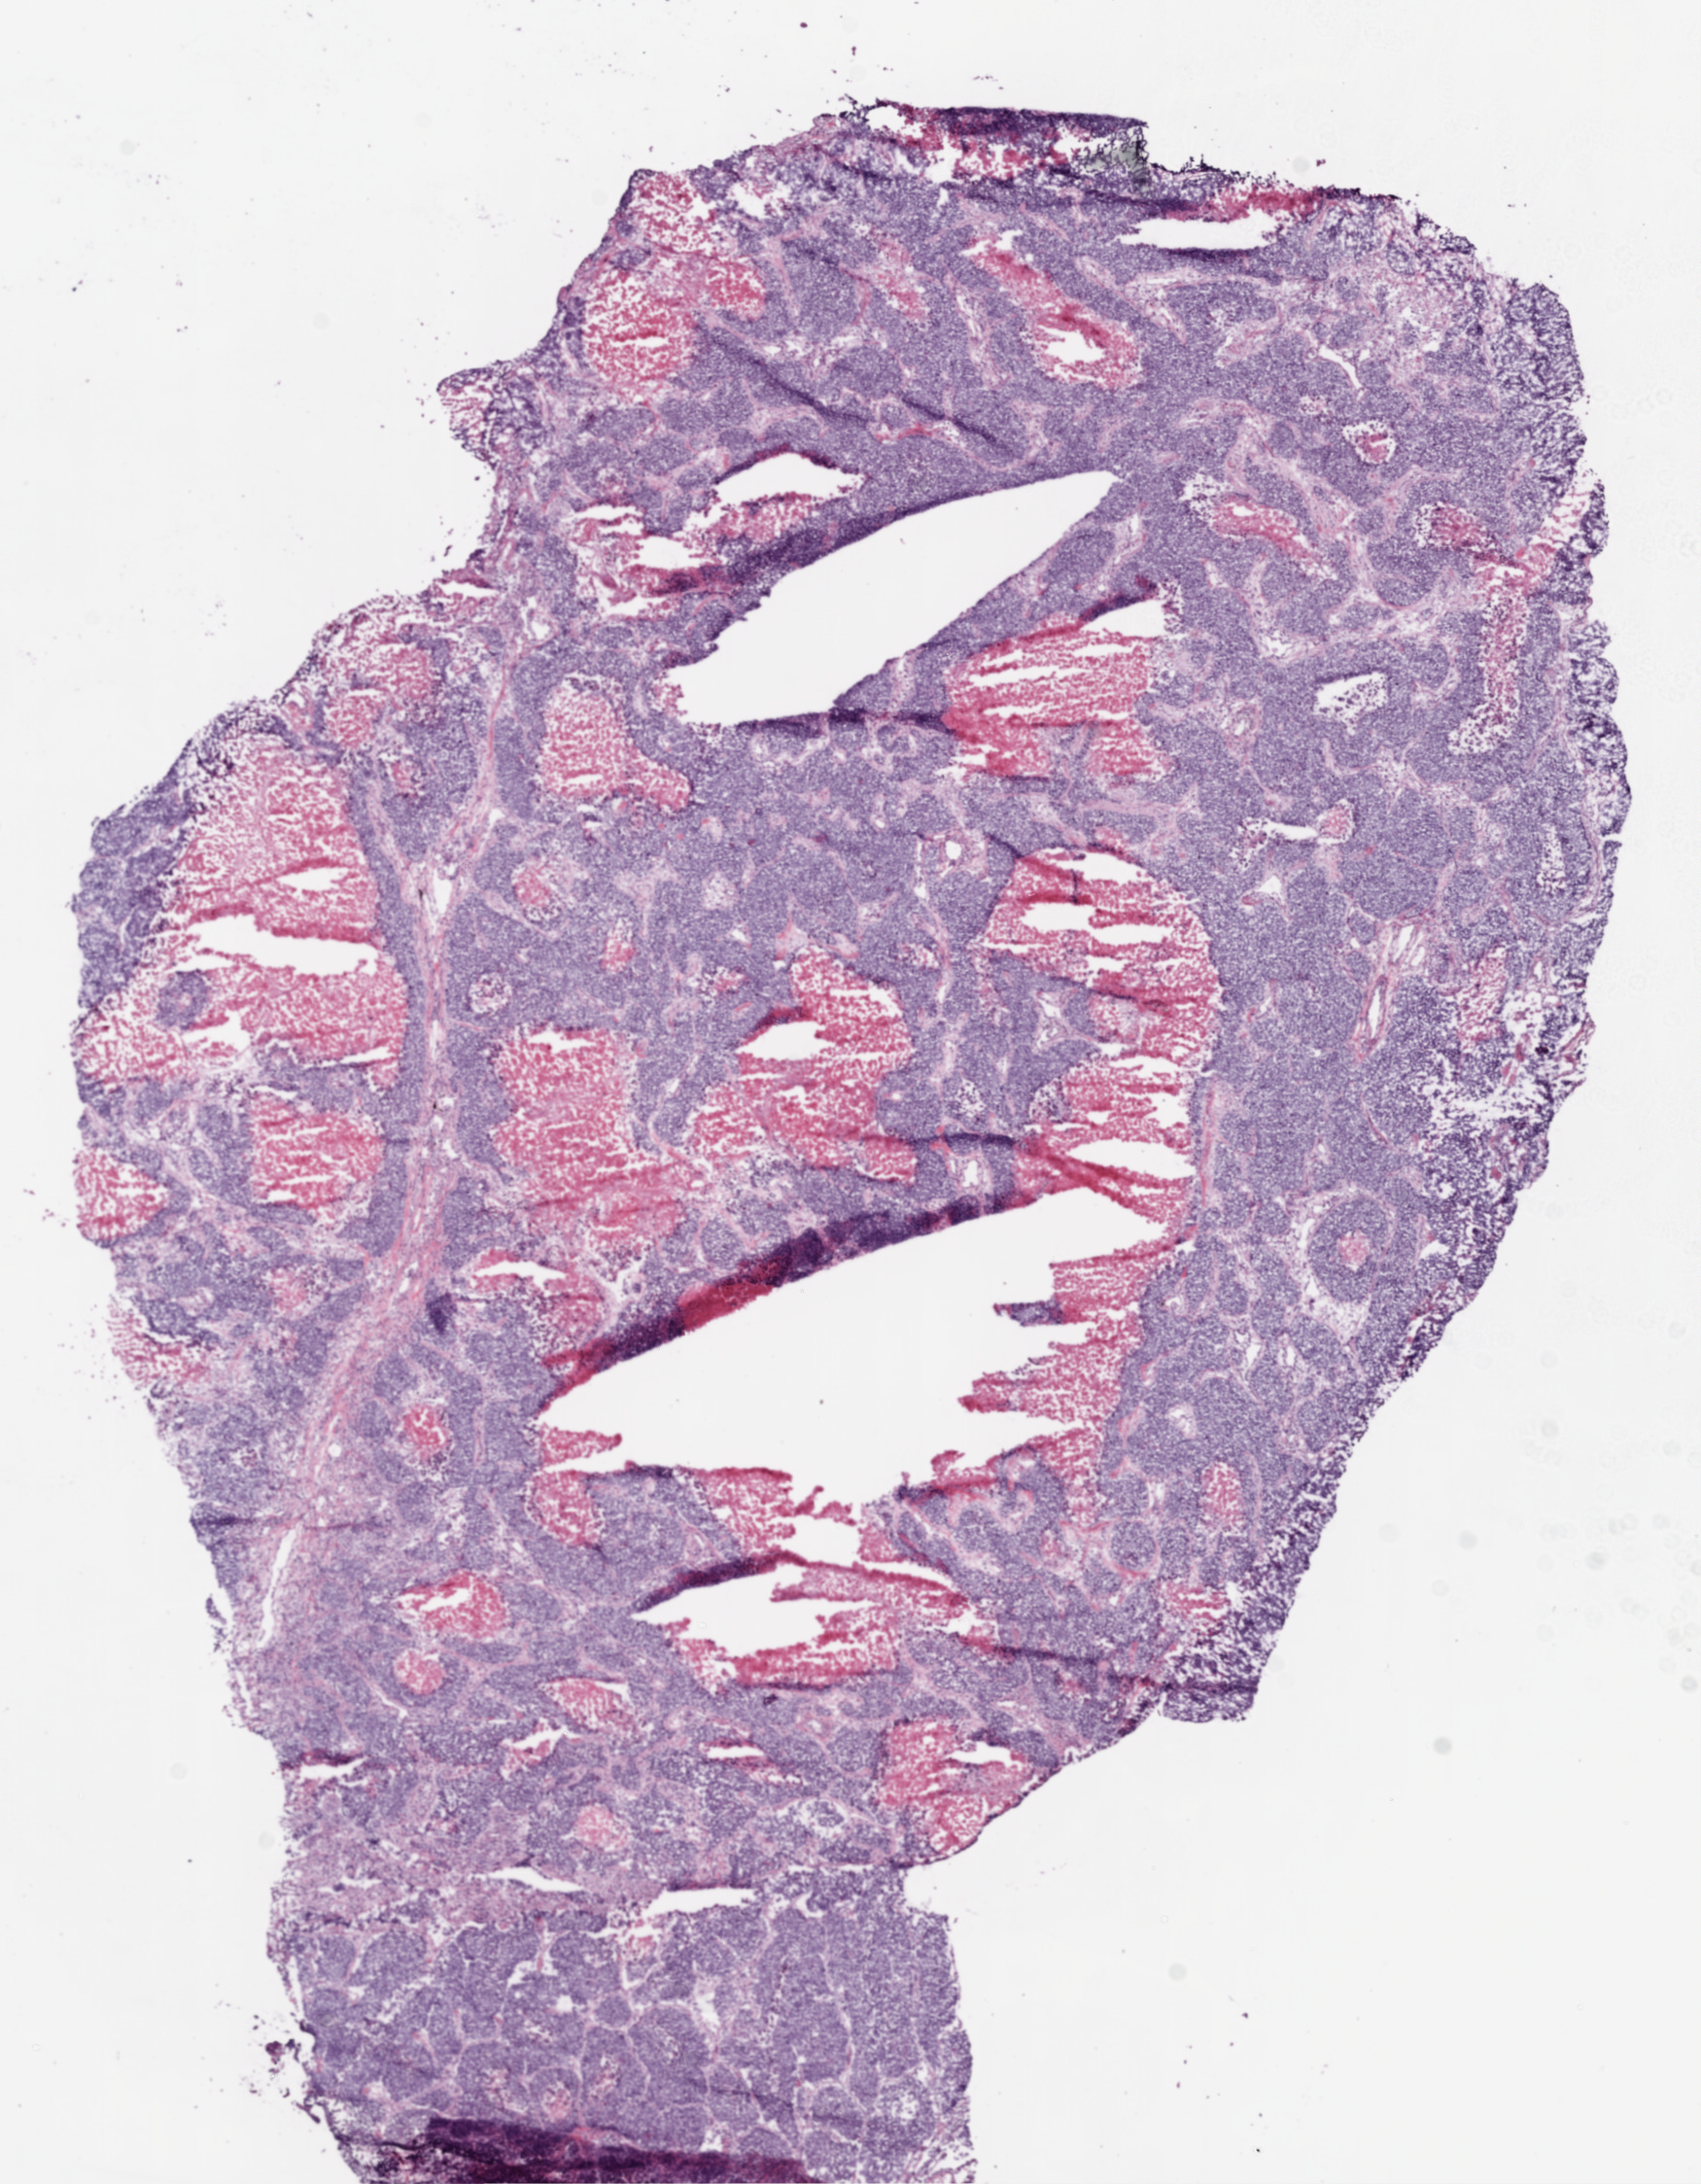
H&E-stained whole-slide image — low-resolution overview of the scanned area, about 7.0 x 9.0 mm. Frozen section. Primary tumour sample from the lung. Patient: female, age at initial diagnosis 63 years. Slide review estimates, as recorded: tumour cells 60%, tumour nuclei 80%, normal cells 0%, stromal cells 10%, necrosis 30%.
- AJCC pathologic stage: IB
- pathologic diagnosis: Squamous cell carcinoma, small cell, nonkeratinizing (middle lobe, lung)
- TNM: T2 N0 MX
- laterality: right